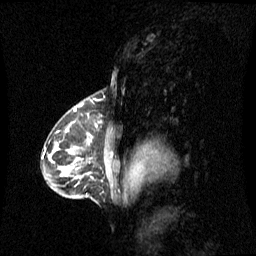
Breast MRI (dynamic contrast-enhanced), one sagittal slice; position 43 of 60 along the scan axis; dynamic contrast-enhanced series, image 2 of 3 at this slice position (ordered by acquisition); 1.5 T; TE 4.2 ms, TR 8.4 ms; 2 mm slice thickness; 256 × 256 image matrix. Female patient, age 42 years. Case-level facts recorded for this patient, not image findings: setting: breast cancer imaged before/during neoadjuvant chemotherapy; receptor status: HR-positive, HER2-negative.
Outlined on this slice (semi-automatically segmented with operator editing):
- analysis volume of interest (the breast-tissue region the enhancement analysis was run in; not a lesion): box from (x=56, y=114) to (x=120, y=182) px
- tumour enhancement mask (voxels above the 70 % enhancement threshold inside the analysis volume of interest): (x=69, y=124)–(x=97, y=154)